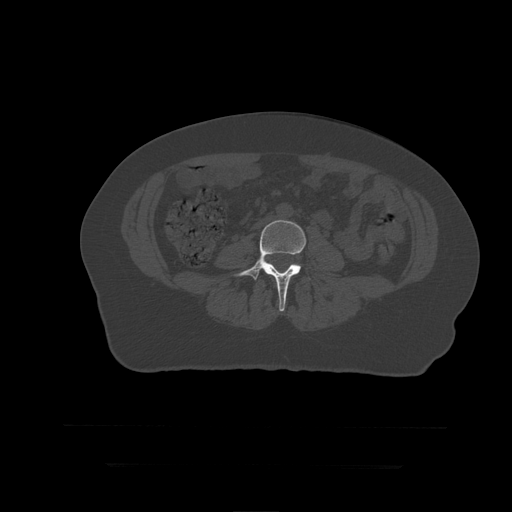
CT including the spine, one axial slice; slice 96 of 399 in the series (ordered by position); 120 kVp; bone window (W 1800 / L 400 HU); 1.25 mm slice thickness; 512 × 512 image matrix. Patient age 41 years. From the clinical record (not read from this slice): primary cancer: breast.
Outlined on this slice (semi-automatic segmentation, software-assisted and operator-edited):
- L4 vertebra: bounding box [x1, y1, x2, y2] px = [234, 220, 311, 312]